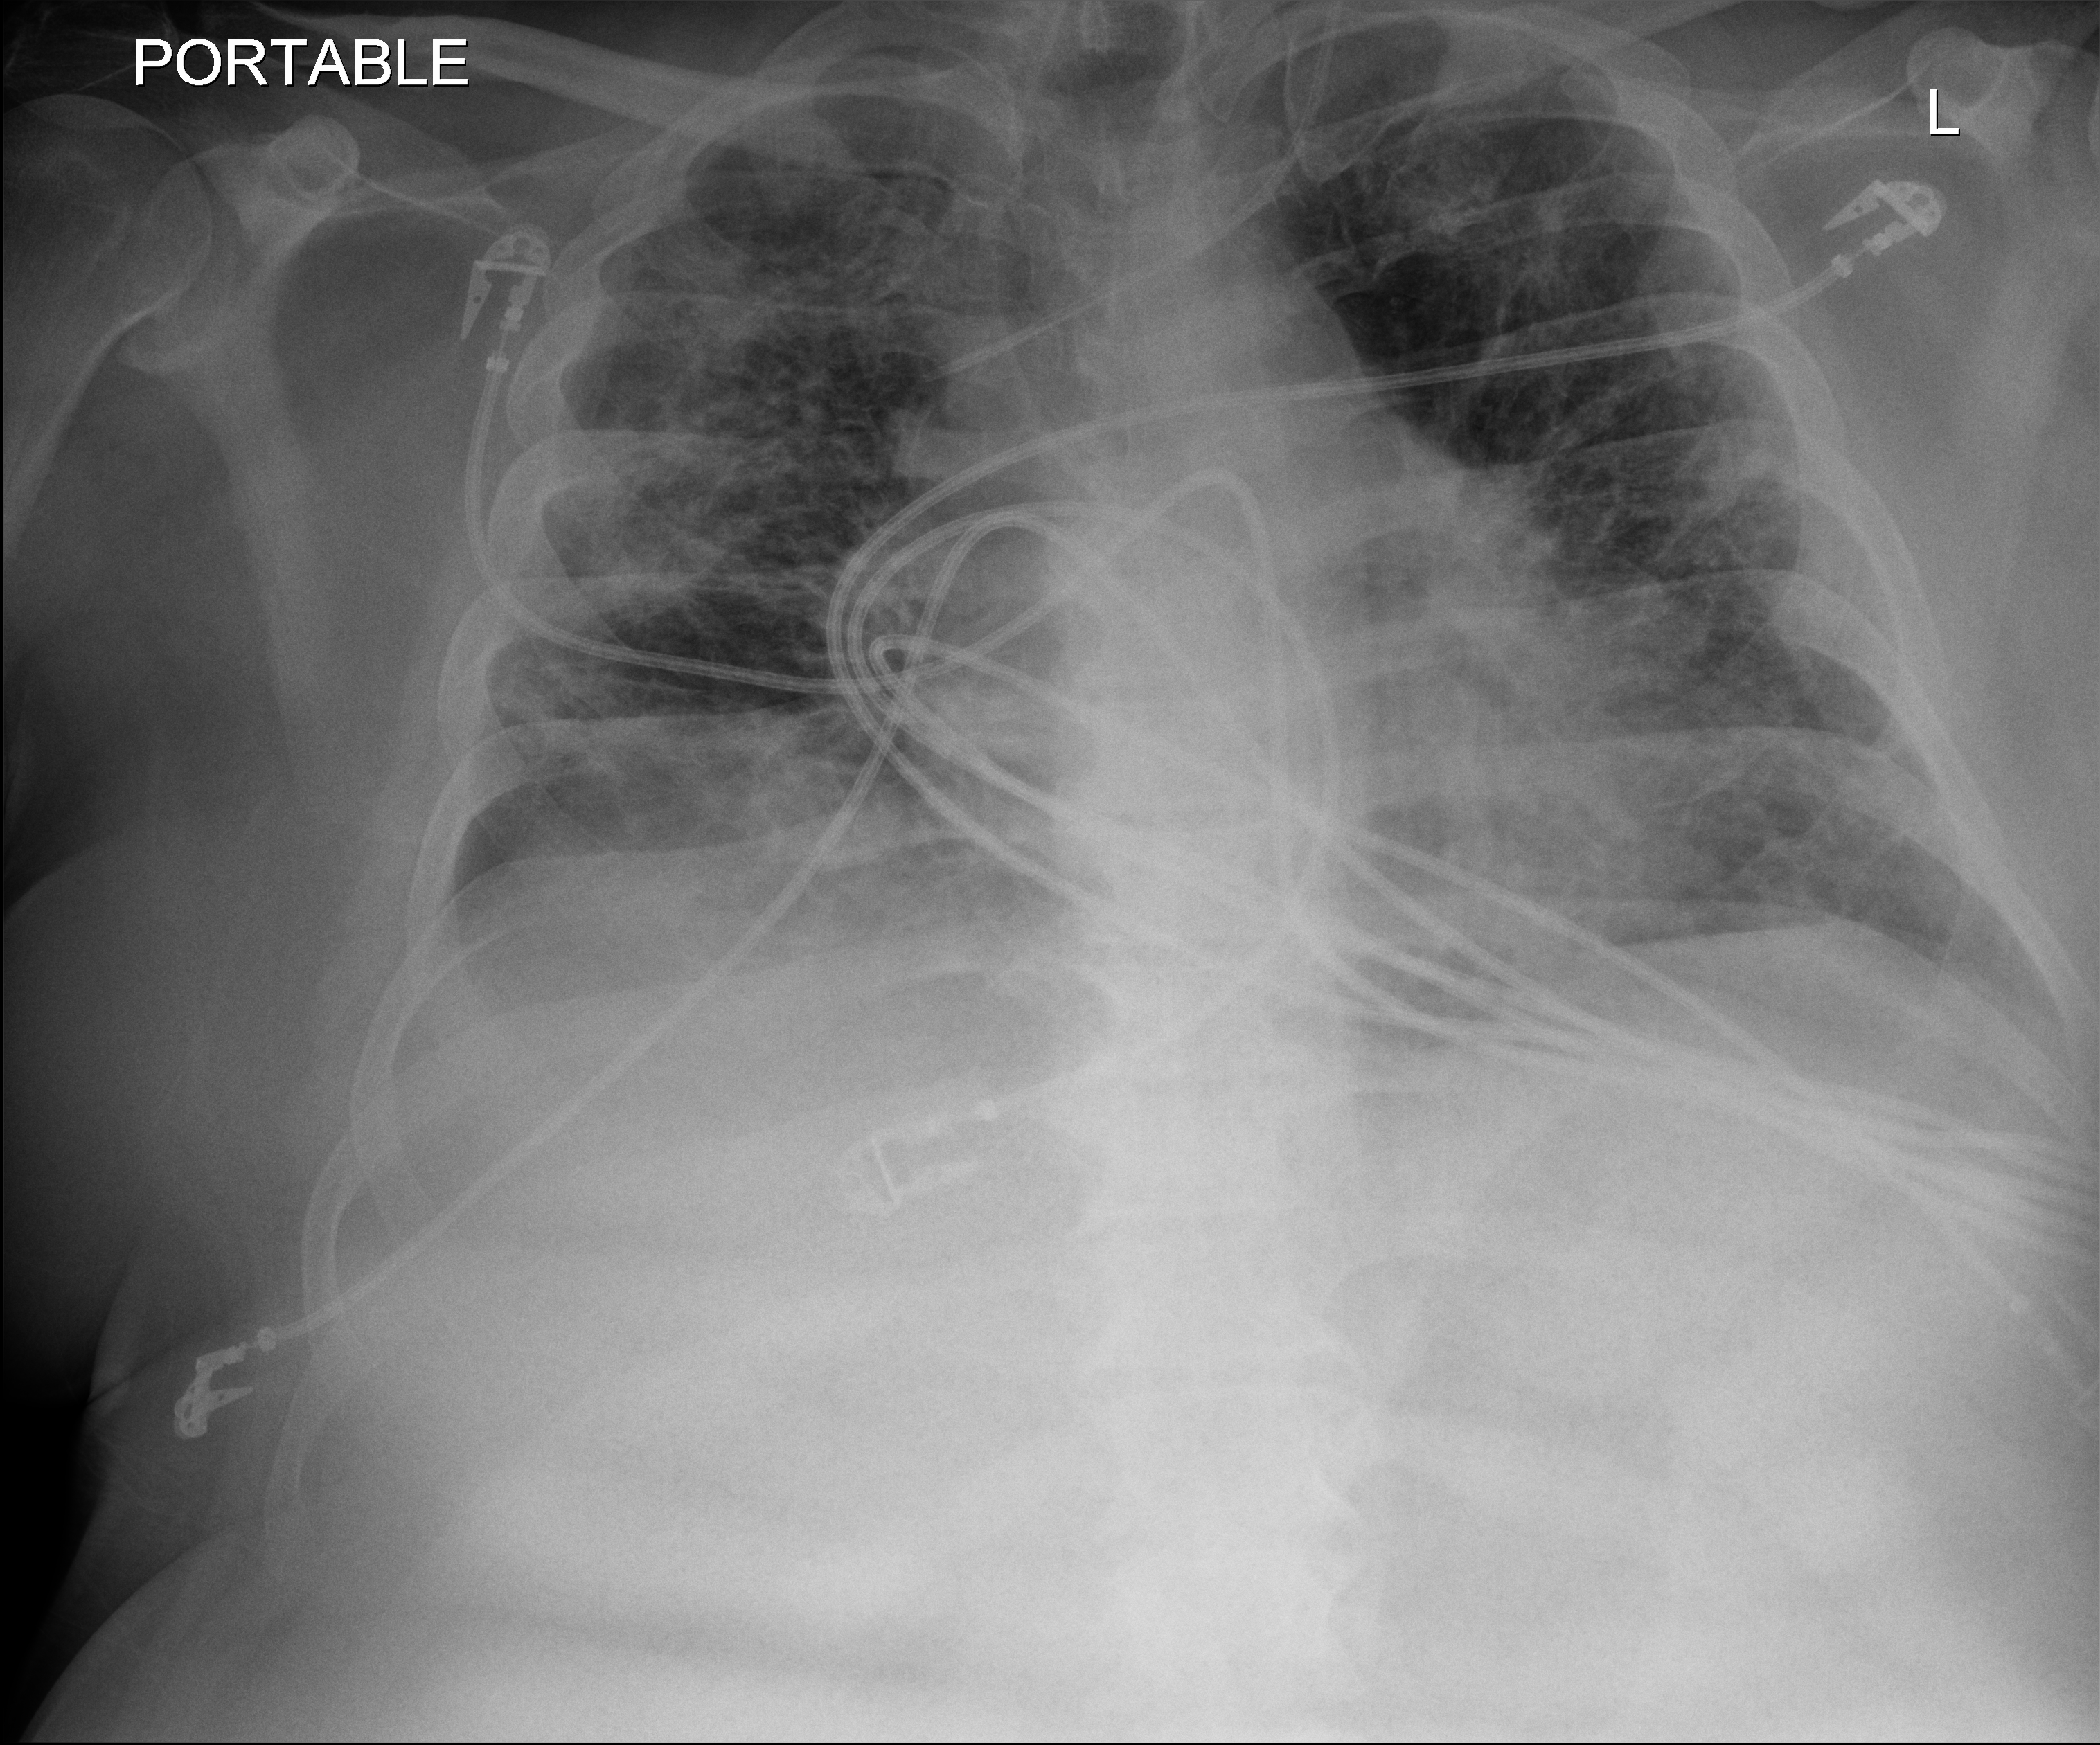
Portable chest radiograph, anteroposterior (AP) projection. Male patient hospitalised with COVID-19, age 18–59 years.
From the hospital-stay record, not from the radiograph (when in the stay this image was taken is not recorded): hypertension (admission record): yes; mechanically ventilated during this hospital stay: yes.